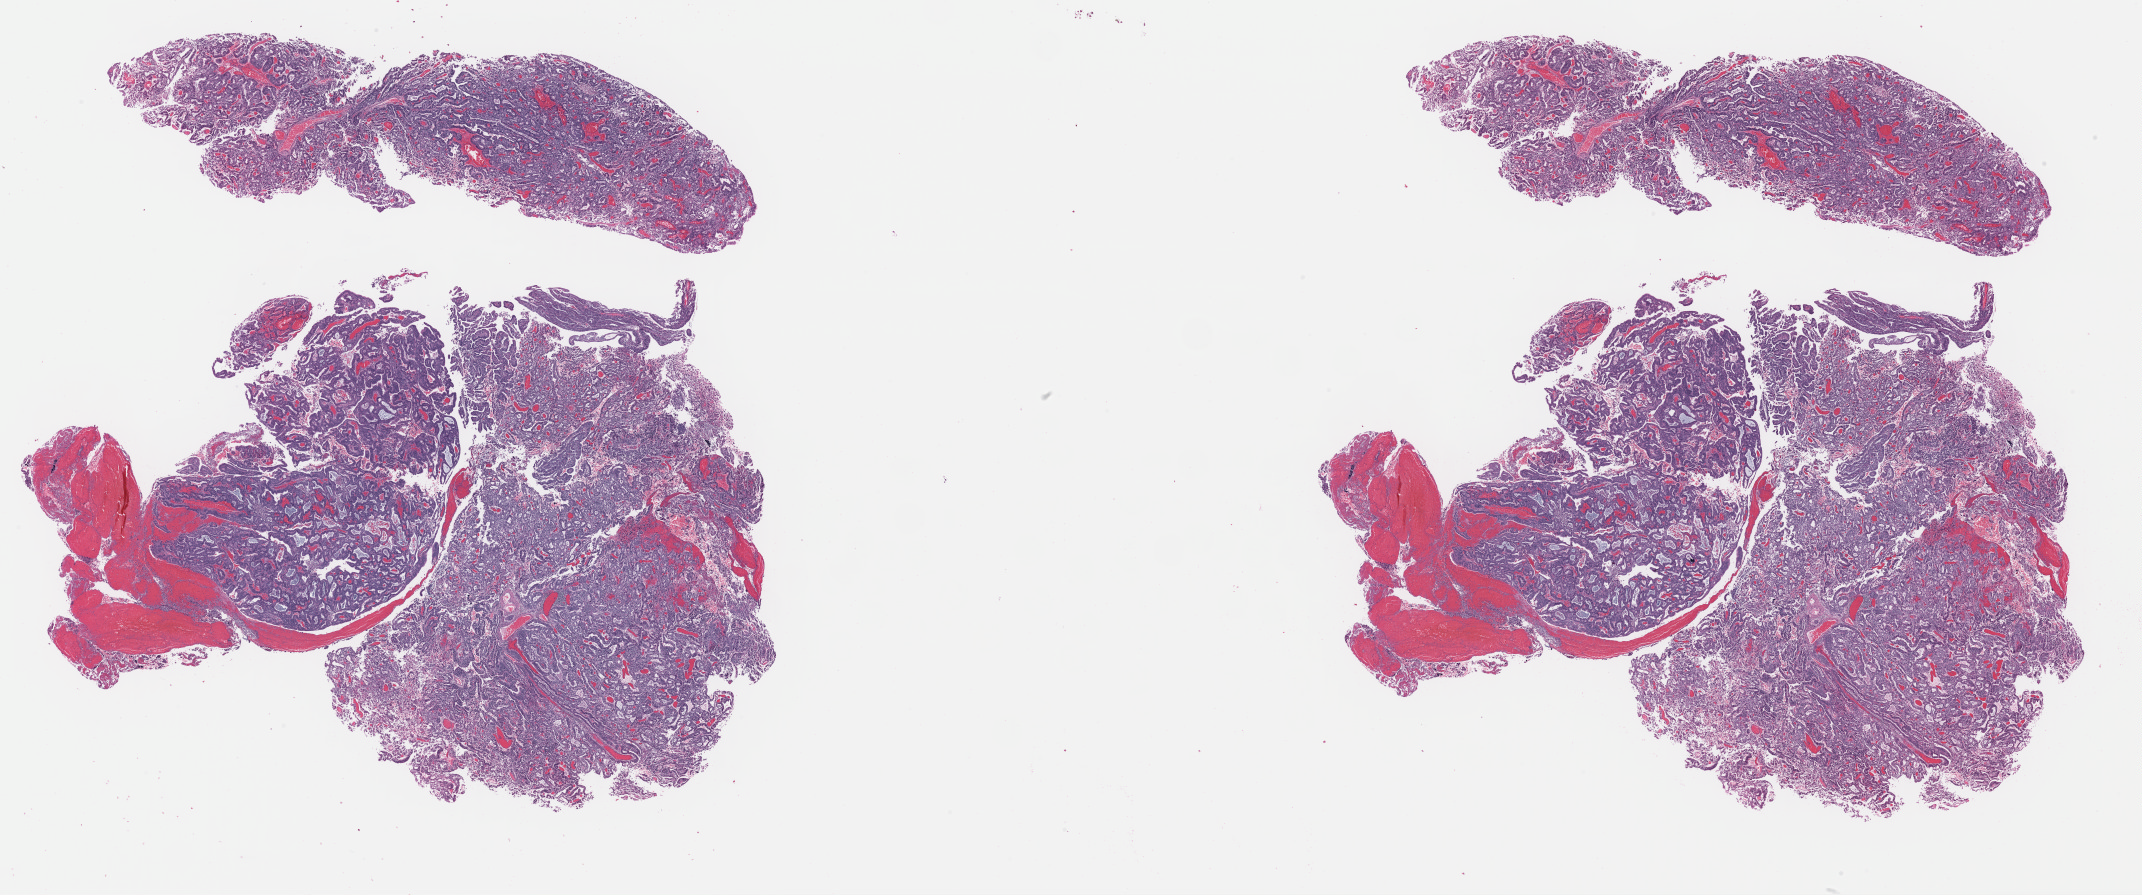
Hematoxylin and eosin (H&E) stained whole-slide image — low-resolution overview of the scanned area, about 33.8 x 14.1 mm, formalin-fixed paraffin-embedded (FFPE) diagnostic section, primary tumour sample from the uterus. Female, age 73 years at initial diagnosis. Histologic grade: G3 (poorly differentiated).
Histologic diagnosis: Endometrioid adenocarcinoma, NOS. FIGO stage: IA.